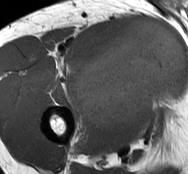
MRI of an extremity soft-tissue mass, one axial slice. Position 53 of 93 along the scan axis. MR volume resampled by the dataset authors to the PET/CT grid (not the native acquisition matrix). 3.27 mm slice thickness. 188 × 174 image matrix, field of view 184 × 170 mm. Male patient. Case-level facts recorded for this patient, not image findings: histological type: undifferentiated - pleiomorphic; grade: high; site of the primary tumour: right thigh.
Annotated regions visible in this slice (expert contour drawn on MRI and transferred to this co-registered scan by the dataset authors):
- gross tumour volume including surrounding oedema: box from (x=74, y=21) to (x=185, y=129) px
- gross tumour volume (mass): (x=75, y=21)–(x=185, y=129)